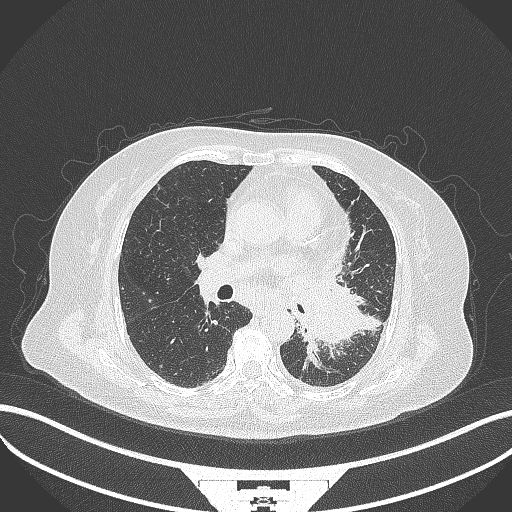
Chest CT, one axial slice. Position 185 of 322 along the scan axis. Lung window (W 1500 / L -600 HU). 1 mm slice thickness. 512 × 512 image matrix. Female patient, age 69 years. Case-level facts recorded for this patient, not image findings: clinical TNM (as recorded): T2b N3 M1.
Structures marked on this image (rectangle marked by the reading radiologist):
- lung tumour (recorded histology: adenocarcinoma): bounding box [x1, y1, x2, y2] px = [301, 280, 365, 351]